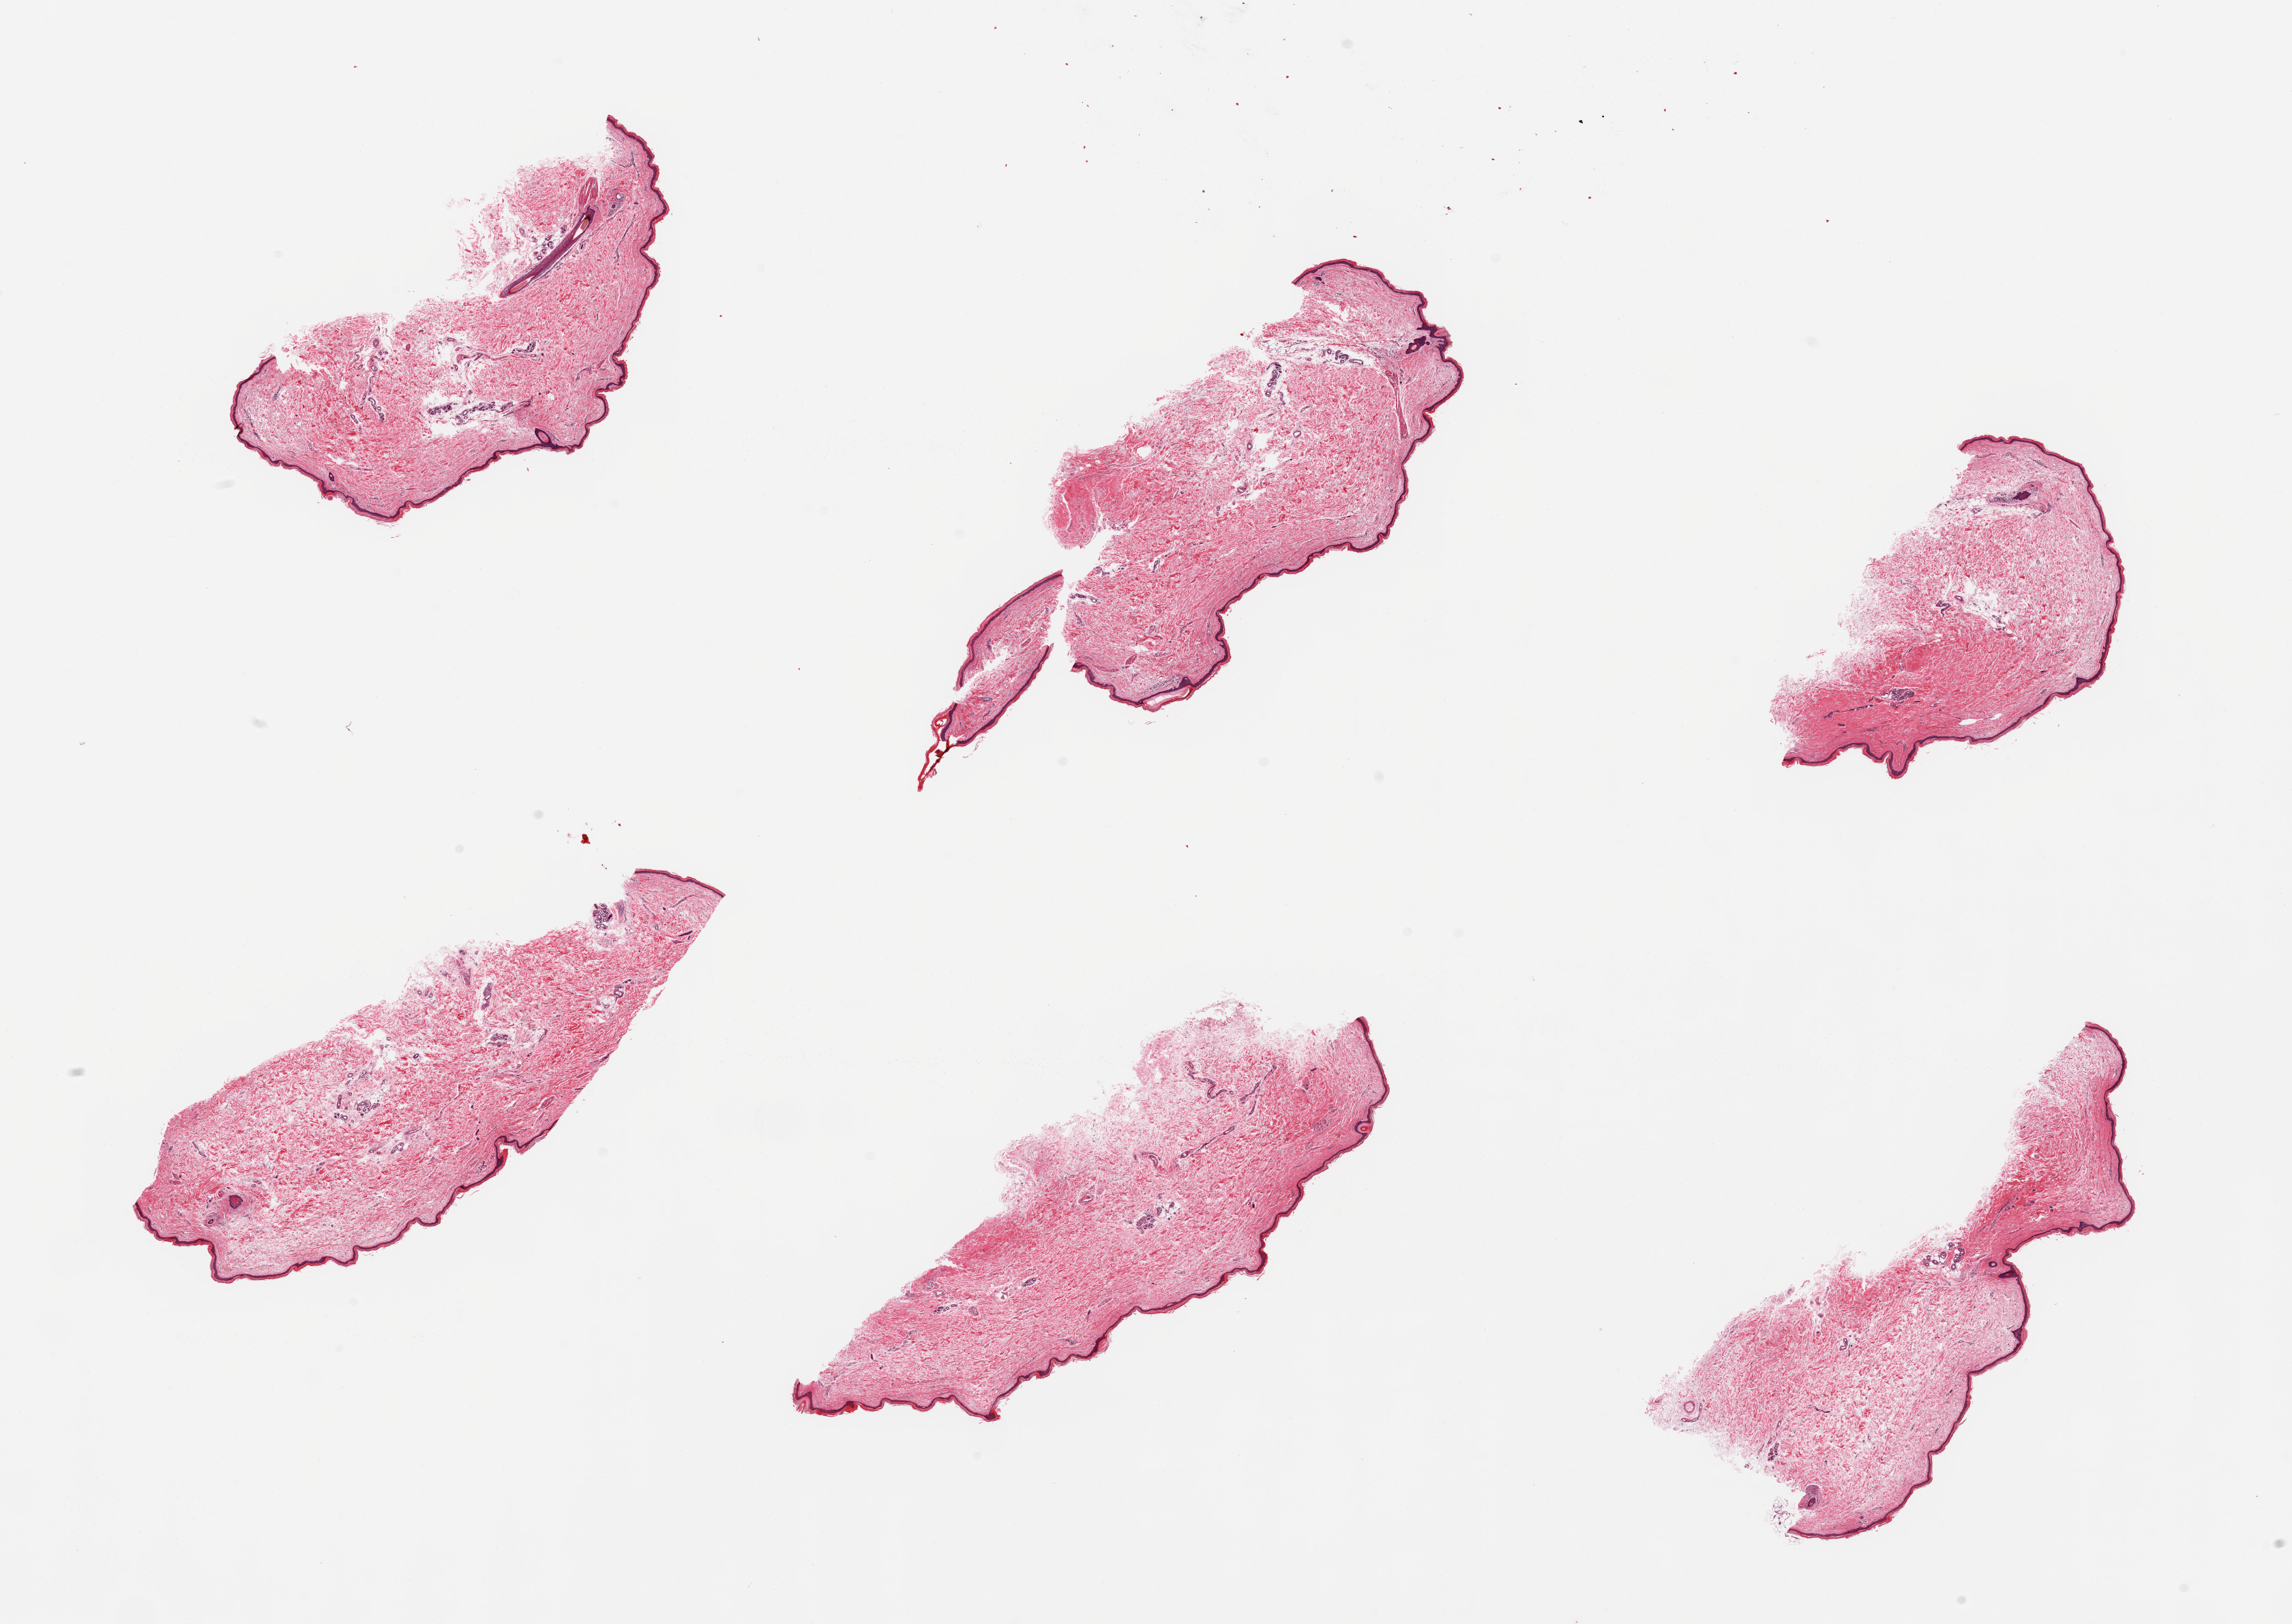
Whole-slide image, H&E stain — low-resolution overview of the scanned area, about 26.6 x 18.8 mm. PAXgene-fixed paraffin-embedded (PFPE) section. Target tissue: skin of lower leg. Donor tissue sample.
- pathologist's review note for this sample: 6 pieces; well trimmed, <5% intradermal fat